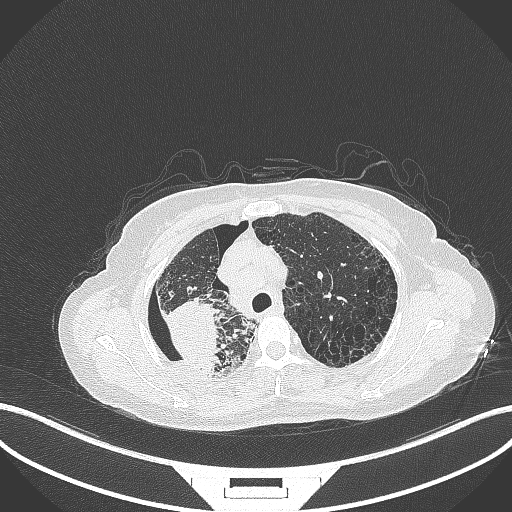
Chest CT, one axial slice. Position 271 of 408 along the scan axis. Reconstruction kernel B70f. 120 kVp. Lung window (W 1500 / L -600 HU). 512 × 512 image matrix, field of view 400 × 400 mm. Female patient, age 64 years. Case-level facts recorded for this patient, not image findings: clinical TNM (as recorded): T3 N3 M0.
Outlined on this slice (bounding box drawn by a radiologist):
- lung tumour (recorded histology: squamous cell carcinoma): bounding box (x1, y1, x2, y2) in pixels: (156, 294, 225, 376)